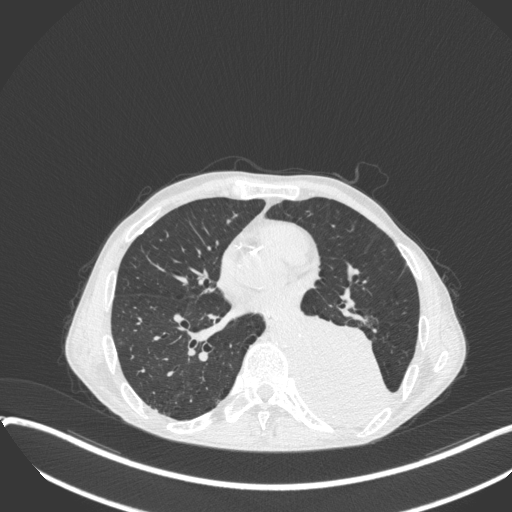
Chest CT, one axial slice. Position 161 of 400 along the scan axis. Reconstruction kernel B31f. 120 kVp. Lung window (W 1500 / L -600 HU). 1 mm slice thickness. 512 × 512 image matrix, field of view 400 × 400 mm. Male patient, age 57 years. Case-level facts recorded for this patient, not image findings: clinical TNM (as recorded): T4 N0 M0.
Outlined on this slice (rectangle marked by the reading radiologist):
- lung tumour (recorded histology: squamous cell carcinoma): bounding box <296,307,395,425> (left, top, right, bottom; pixels)